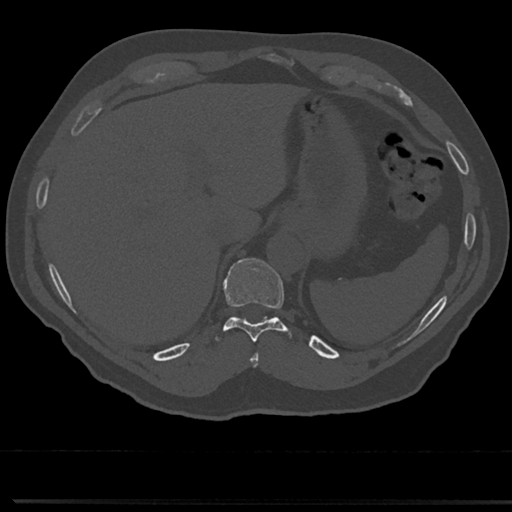
CT including the spine, one axial slice; slice 252 of 817 in the series (ordered by position); reconstruction kernel Br40s/3; 120 kVp; bone window (W 1800 / L 400 HU); 0.5 mm slice thickness; 512 × 512 image matrix, field of view 355 × 355 mm. Male patient, age 61 years. Case-level facts recorded for this patient, not image findings: primary cancer: prostate.
Structures marked on this image (semi-automatic segmentation, software-assisted and operator-edited):
- T10 vertebra: bounding box [x1, y1, x2, y2] px = [213, 258, 296, 344]
- T9 vertebra: [250, 349, 260, 368]